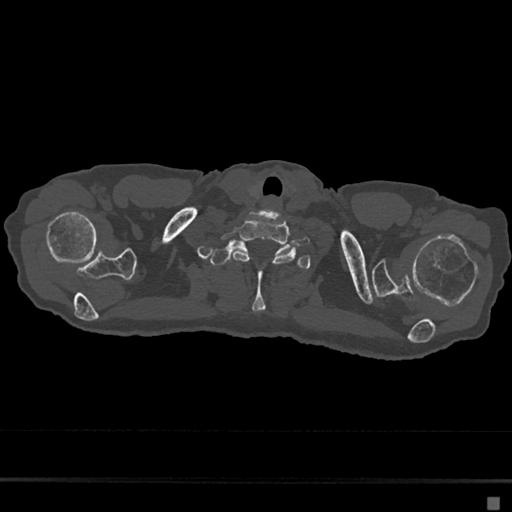
CT including the spine, one axial slice. Position 628 of 797 along the scan axis. Bone window (W 1800 / L 400 HU). 0.5 mm slice thickness. 512 × 512 image matrix, field of view 360 × 360 mm. Female patient, age 68 years. From the clinical record (not read from this slice): primary cancer: renal.
Structures marked on this image (semi-automatic segmentation, software-assisted and operator-edited):
- T1 vertebra: bounding box (x1, y1, x2, y2) in pixels: (209, 241, 311, 313)